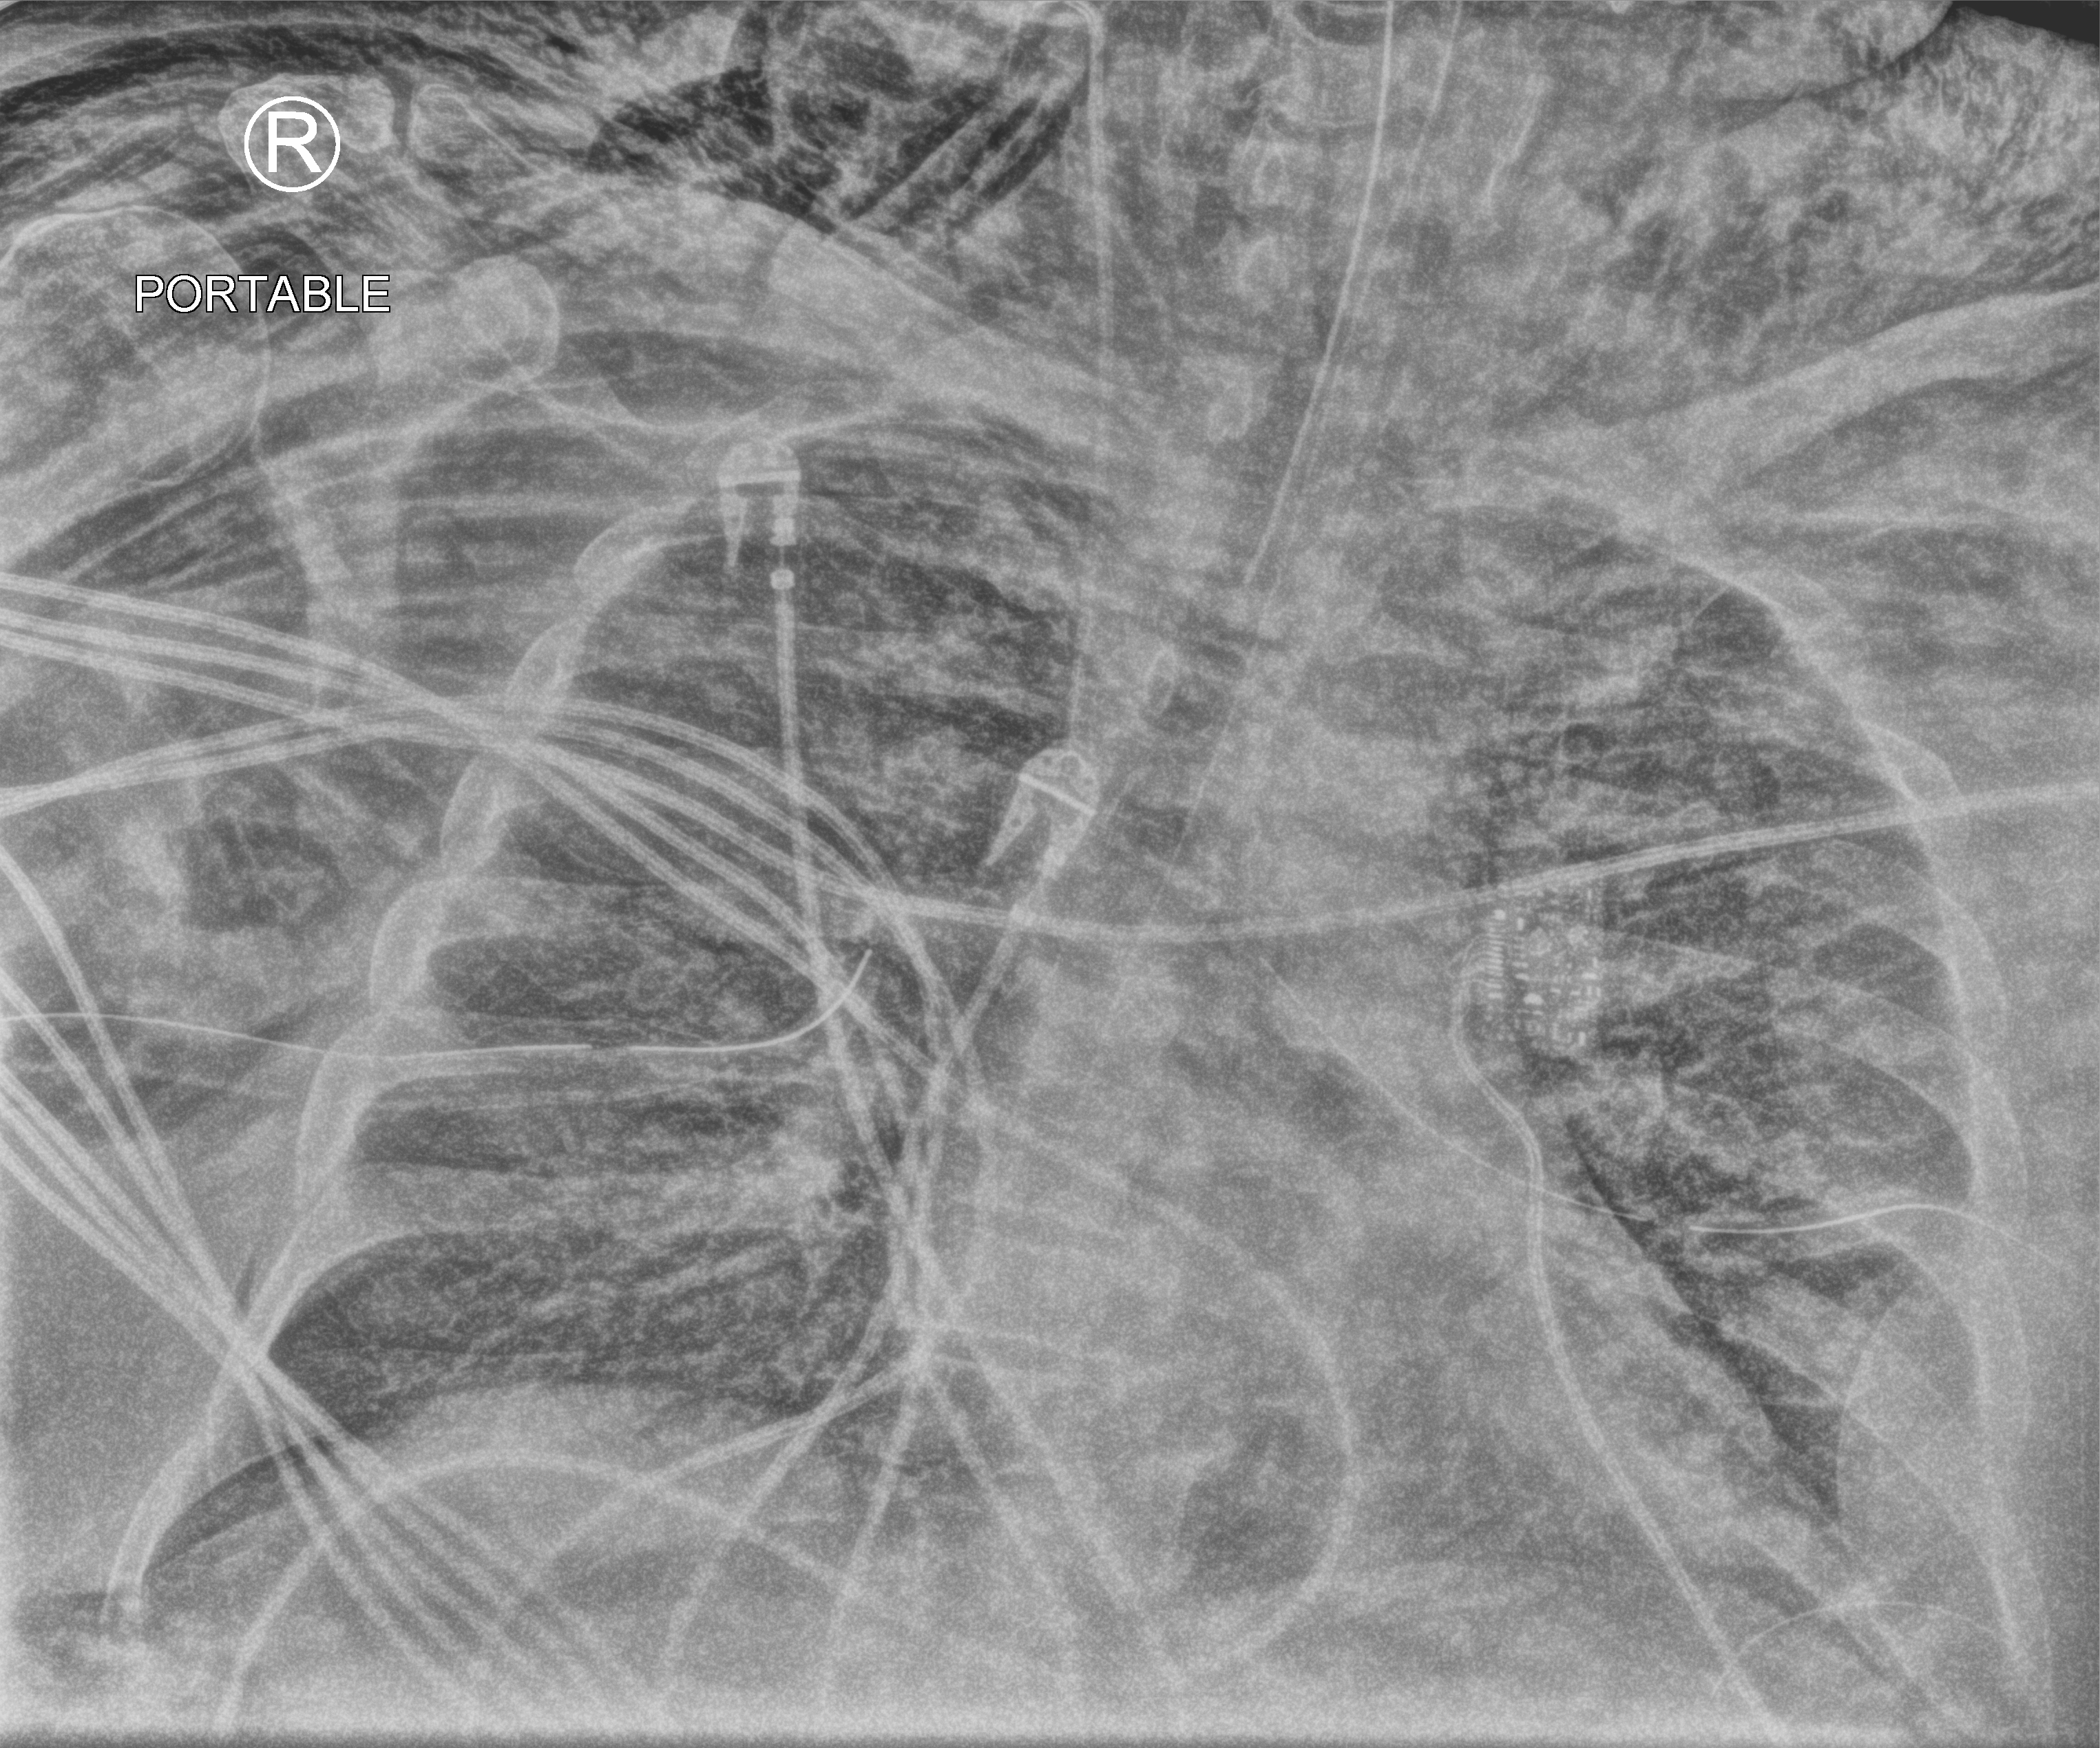
Bedside chest radiograph (computed radiography); anteroposterior (AP) projection. Adult patient hospitalised with COVID-19, age 18–59 years.
From the hospital-stay record, not from the radiograph (when in the stay this image was taken is not recorded): chronic kidney disease (admission record): no; mechanically ventilated during this hospital stay: yes.